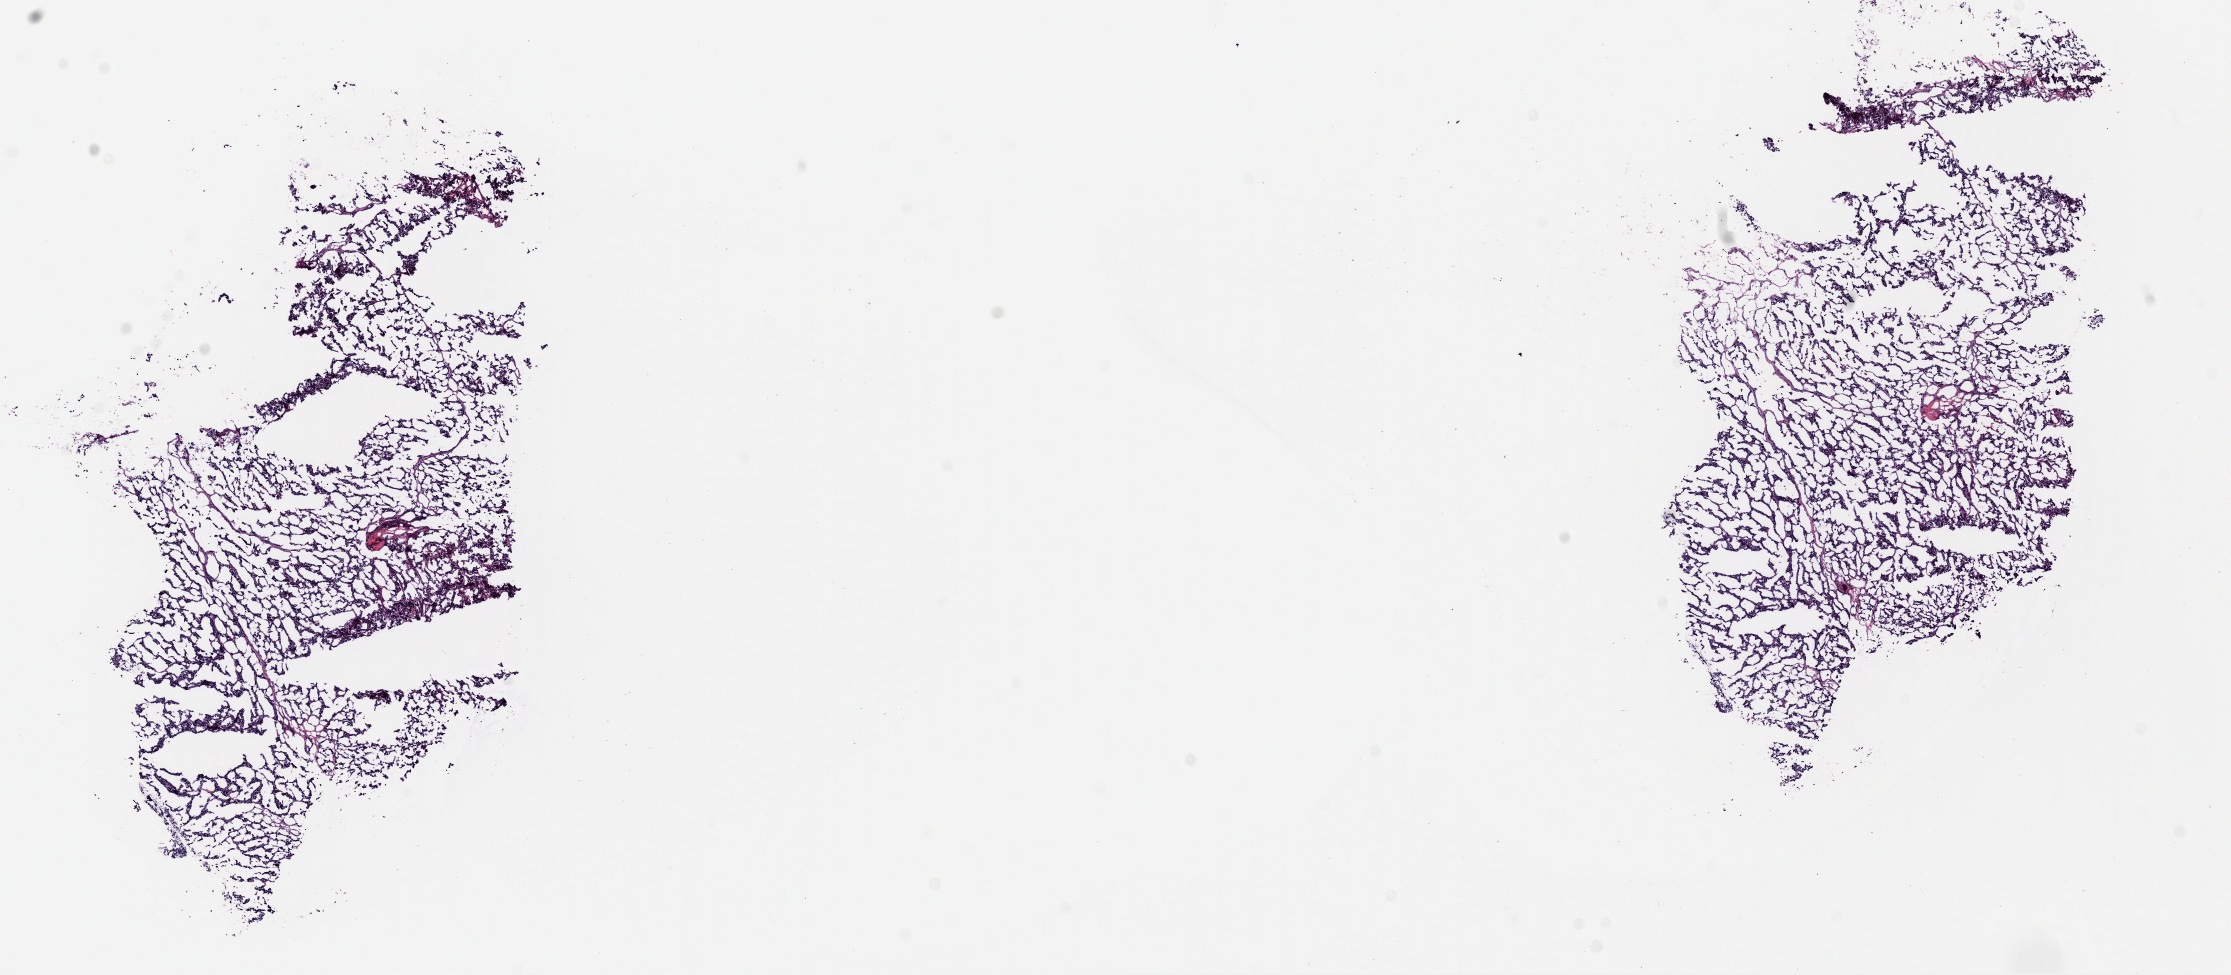
Whole-slide histology image, H&E-stained — a low-resolution overview of the entire scanned area, about 17.6 x 7.7 mm; frozen section from the top of the tissue portion; metastatic tumour sample. Female, age 75 years at initial diagnosis.
This section: metastatic tumour tissue. Patient diagnosis: Malignant melanoma, NOS.